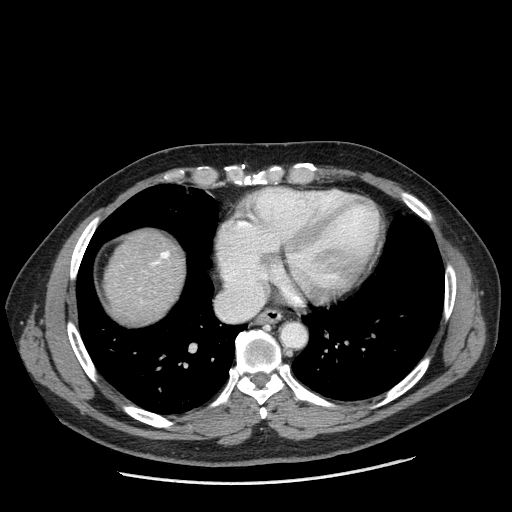
Contrast-enhanced abdominal CT (liver protocol), one axial slice. Position 179 of 198 along the scan axis. One of 2 acquisitions stored at this slice position. Soft-tissue window (W 400 / L 40 HU). 512 × 512 image matrix, field of view 400 × 400 mm. Case-level facts recorded for this patient, not image findings: diagnosis: hepatocellular carcinoma (patient treated with transarterial chemoembolisation; whether this scan precedes or follows treatment is not stated here); TNM stage (as recorded): Stage-II; Child-Pugh class: A; tumour nodularity: multinodular.
Annotated regions visible in this slice (semi-automatically segmented with operator editing):
- liver parenchyma outside the tumour (the mass and vessels are separate outlines, so this box may not span the whole liver): box from (x=104, y=230) to (x=184, y=322) px
- liver vessels: (x=139, y=251)–(x=170, y=290)